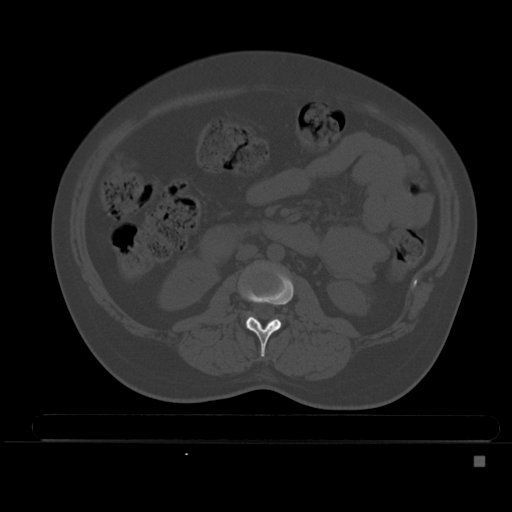
CT including the spine, one axial slice. Position 166 of 495 along the scan axis. Bone window (W 1800 / L 400 HU). 1.5 mm slice thickness. 512 × 512 image matrix, field of view 404 × 404 mm. Patient: female, 33 years. Case-level facts recorded for this patient, not image findings: primary cancer: breast.
Structures marked on this image (semi-automatic segmentation, software-assisted and operator-edited):
- L2 vertebra: bounding box <239,267,294,357> (left, top, right, bottom; pixels)